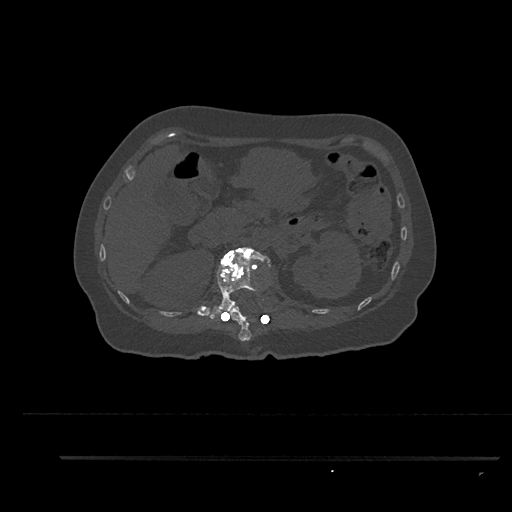
CT including the spine, one axial slice. Slice 232 of 797 in the series (ordered by position). Reconstruction kernel Br40s/3. Bone window (W 1800 / L 400 HU). 512 × 512 image matrix, field of view 408 × 408 mm. Patient: female, 44 years. From the clinical record (not read from this slice): primary cancer: renal; vertebrae with lytic lesions (as recorded): L1.
Annotated regions visible in this slice (semi-automatic segmentation, software-assisted and operator-edited):
- L1 vertebra: bounding box (x1, y1, x2, y2) in pixels: (208, 247, 271, 321)
- T12 vertebra: (220, 307, 253, 341)